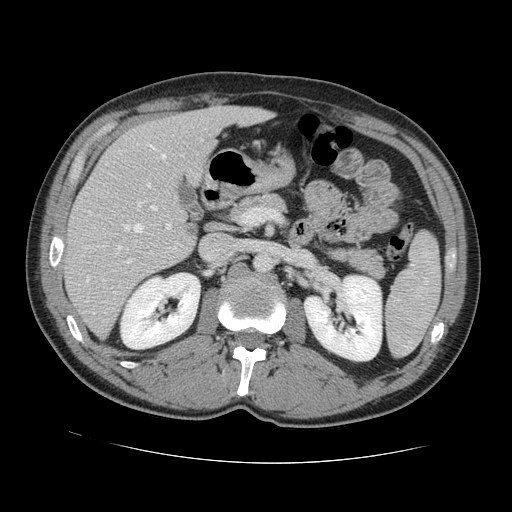
Contrast-enhanced abdominal CT, one axial slice; slice 70 of 131 in the series (ordered by position); intravenous contrast given; soft-tissue window (W 400 / L 40 HU); 512 × 512 image matrix, field of view 380 × 380 mm. Male patient, age 40 years. From the clinical record (not read from this slice): diagnosis: colorectal cancer liver metastases, imaged before liver resection; multiple liver metastases: yes; largest metastasis: 2.9 cm; disease in both lobes: yes.
Structures marked on this image (outlined manually by an expert reader):
- hepatic veins: bounding box [x1, y1, x2, y2] px = [86, 143, 167, 282]
- liver: [66, 107, 267, 336]
- planned liver remnant (the part of the liver to remain after resection): [108, 107, 267, 190]
- portal vein (with intrahepatic branches): [124, 182, 172, 264]
- liver metastasis: [190, 228, 195, 235]